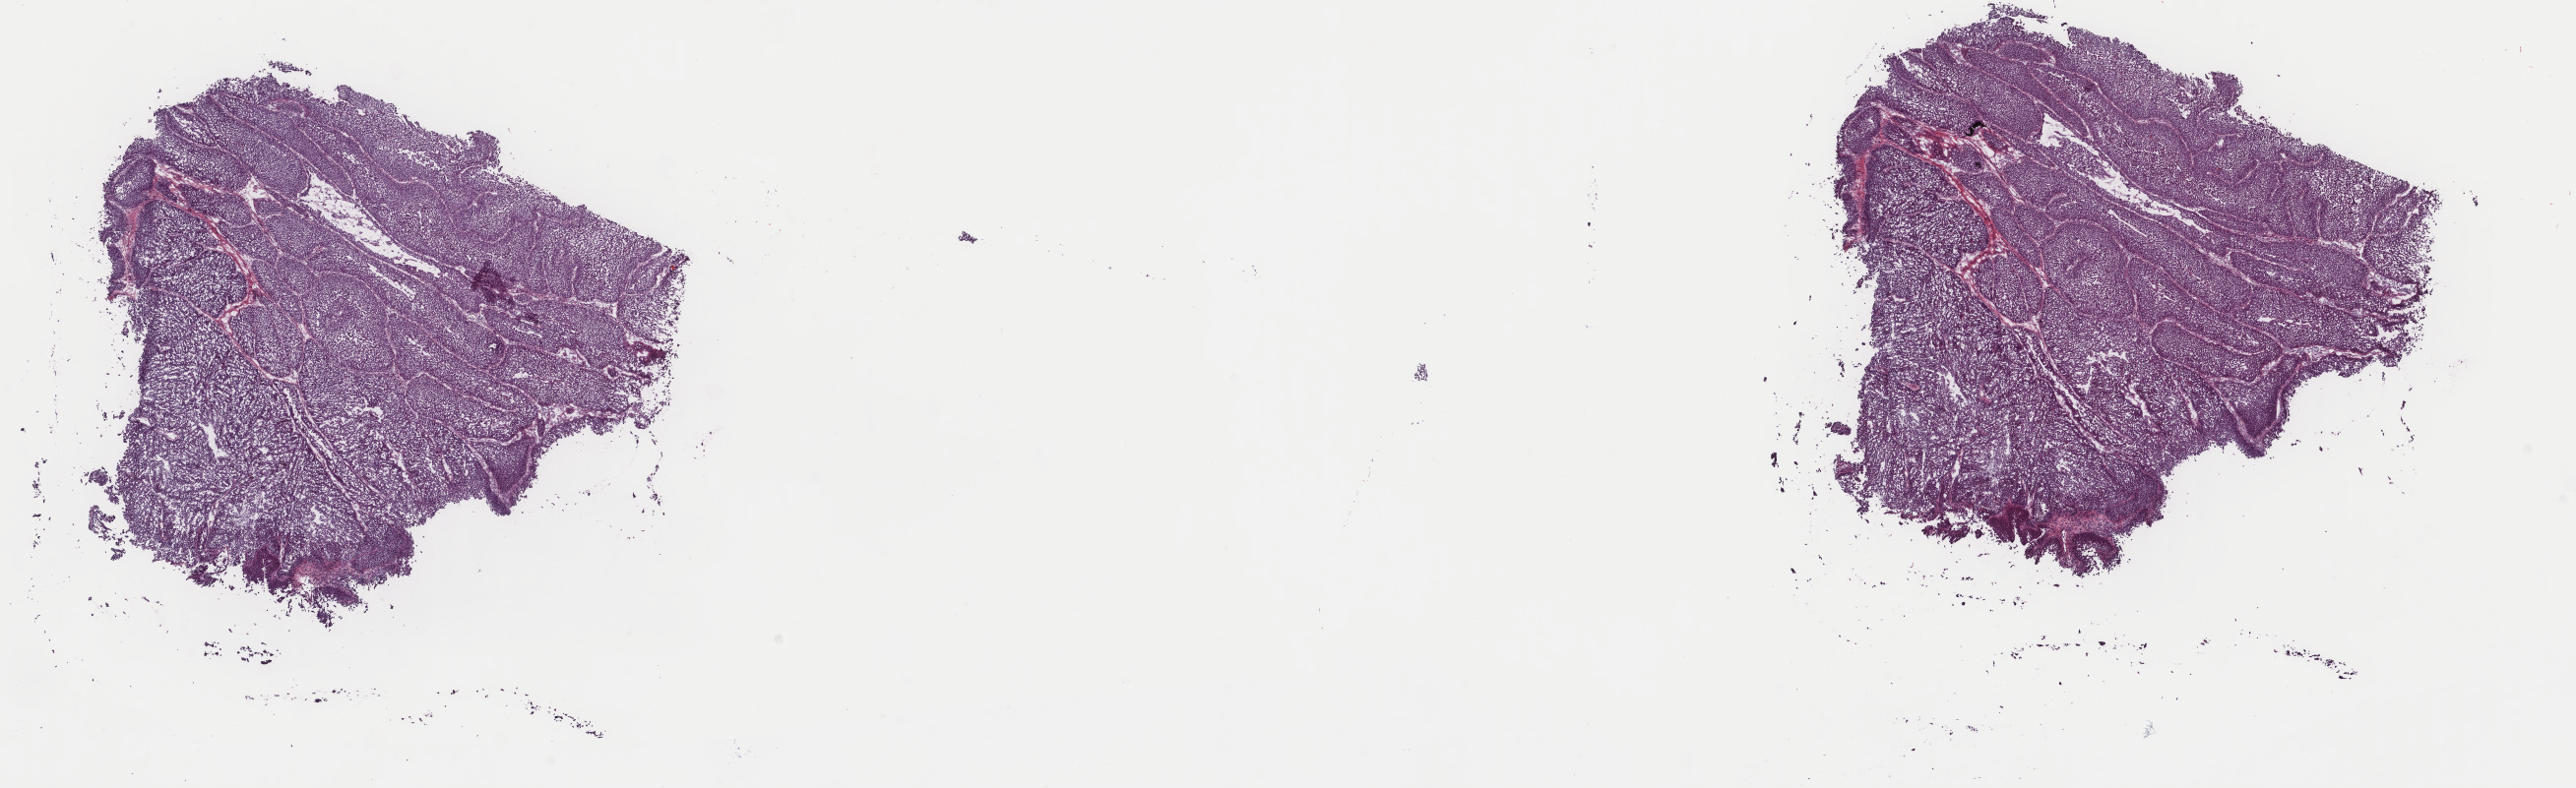
Digitized Hematoxylin and eosin (H&E) stained tissue section (whole slide), shown as a low-resolution overview of the whole scanned area (about 20.8 x 6.4 mm). Frozen section from the top of the tissue portion. Sample: primary tumour, bladder. Male, age 41 years at initial diagnosis. Histologic grade: low grade. Composition of this section per pathologist review: tumour cells 100%, tumour nuclei 85%, normal cells 0%, stromal cells 0%, necrosis 0%. Infiltration values recorded for this section: lymphocyte infiltration 1%, monocyte infiltration 0%, neutrophil infiltration 0%.
* pathologic diagnosis: Papillary transitional cell carcinoma
* AJCC pathologic stage: II